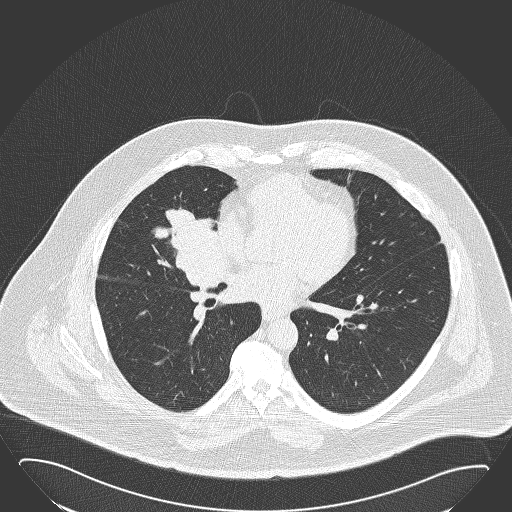
Low-dose screening chest CT, one axial slice; position 76 of 168 along the scan axis; lung window (W 1500 / L -600 HU); 2 mm slice thickness; 512 × 512 image matrix, field of view 432 × 432 mm.
Structures marked on this image (manually delineated by an expert):
- lesion 1 (tumor, hilum of right lung): bounding box (x1, y1, x2, y2) in pixels: (155, 208, 226, 293)